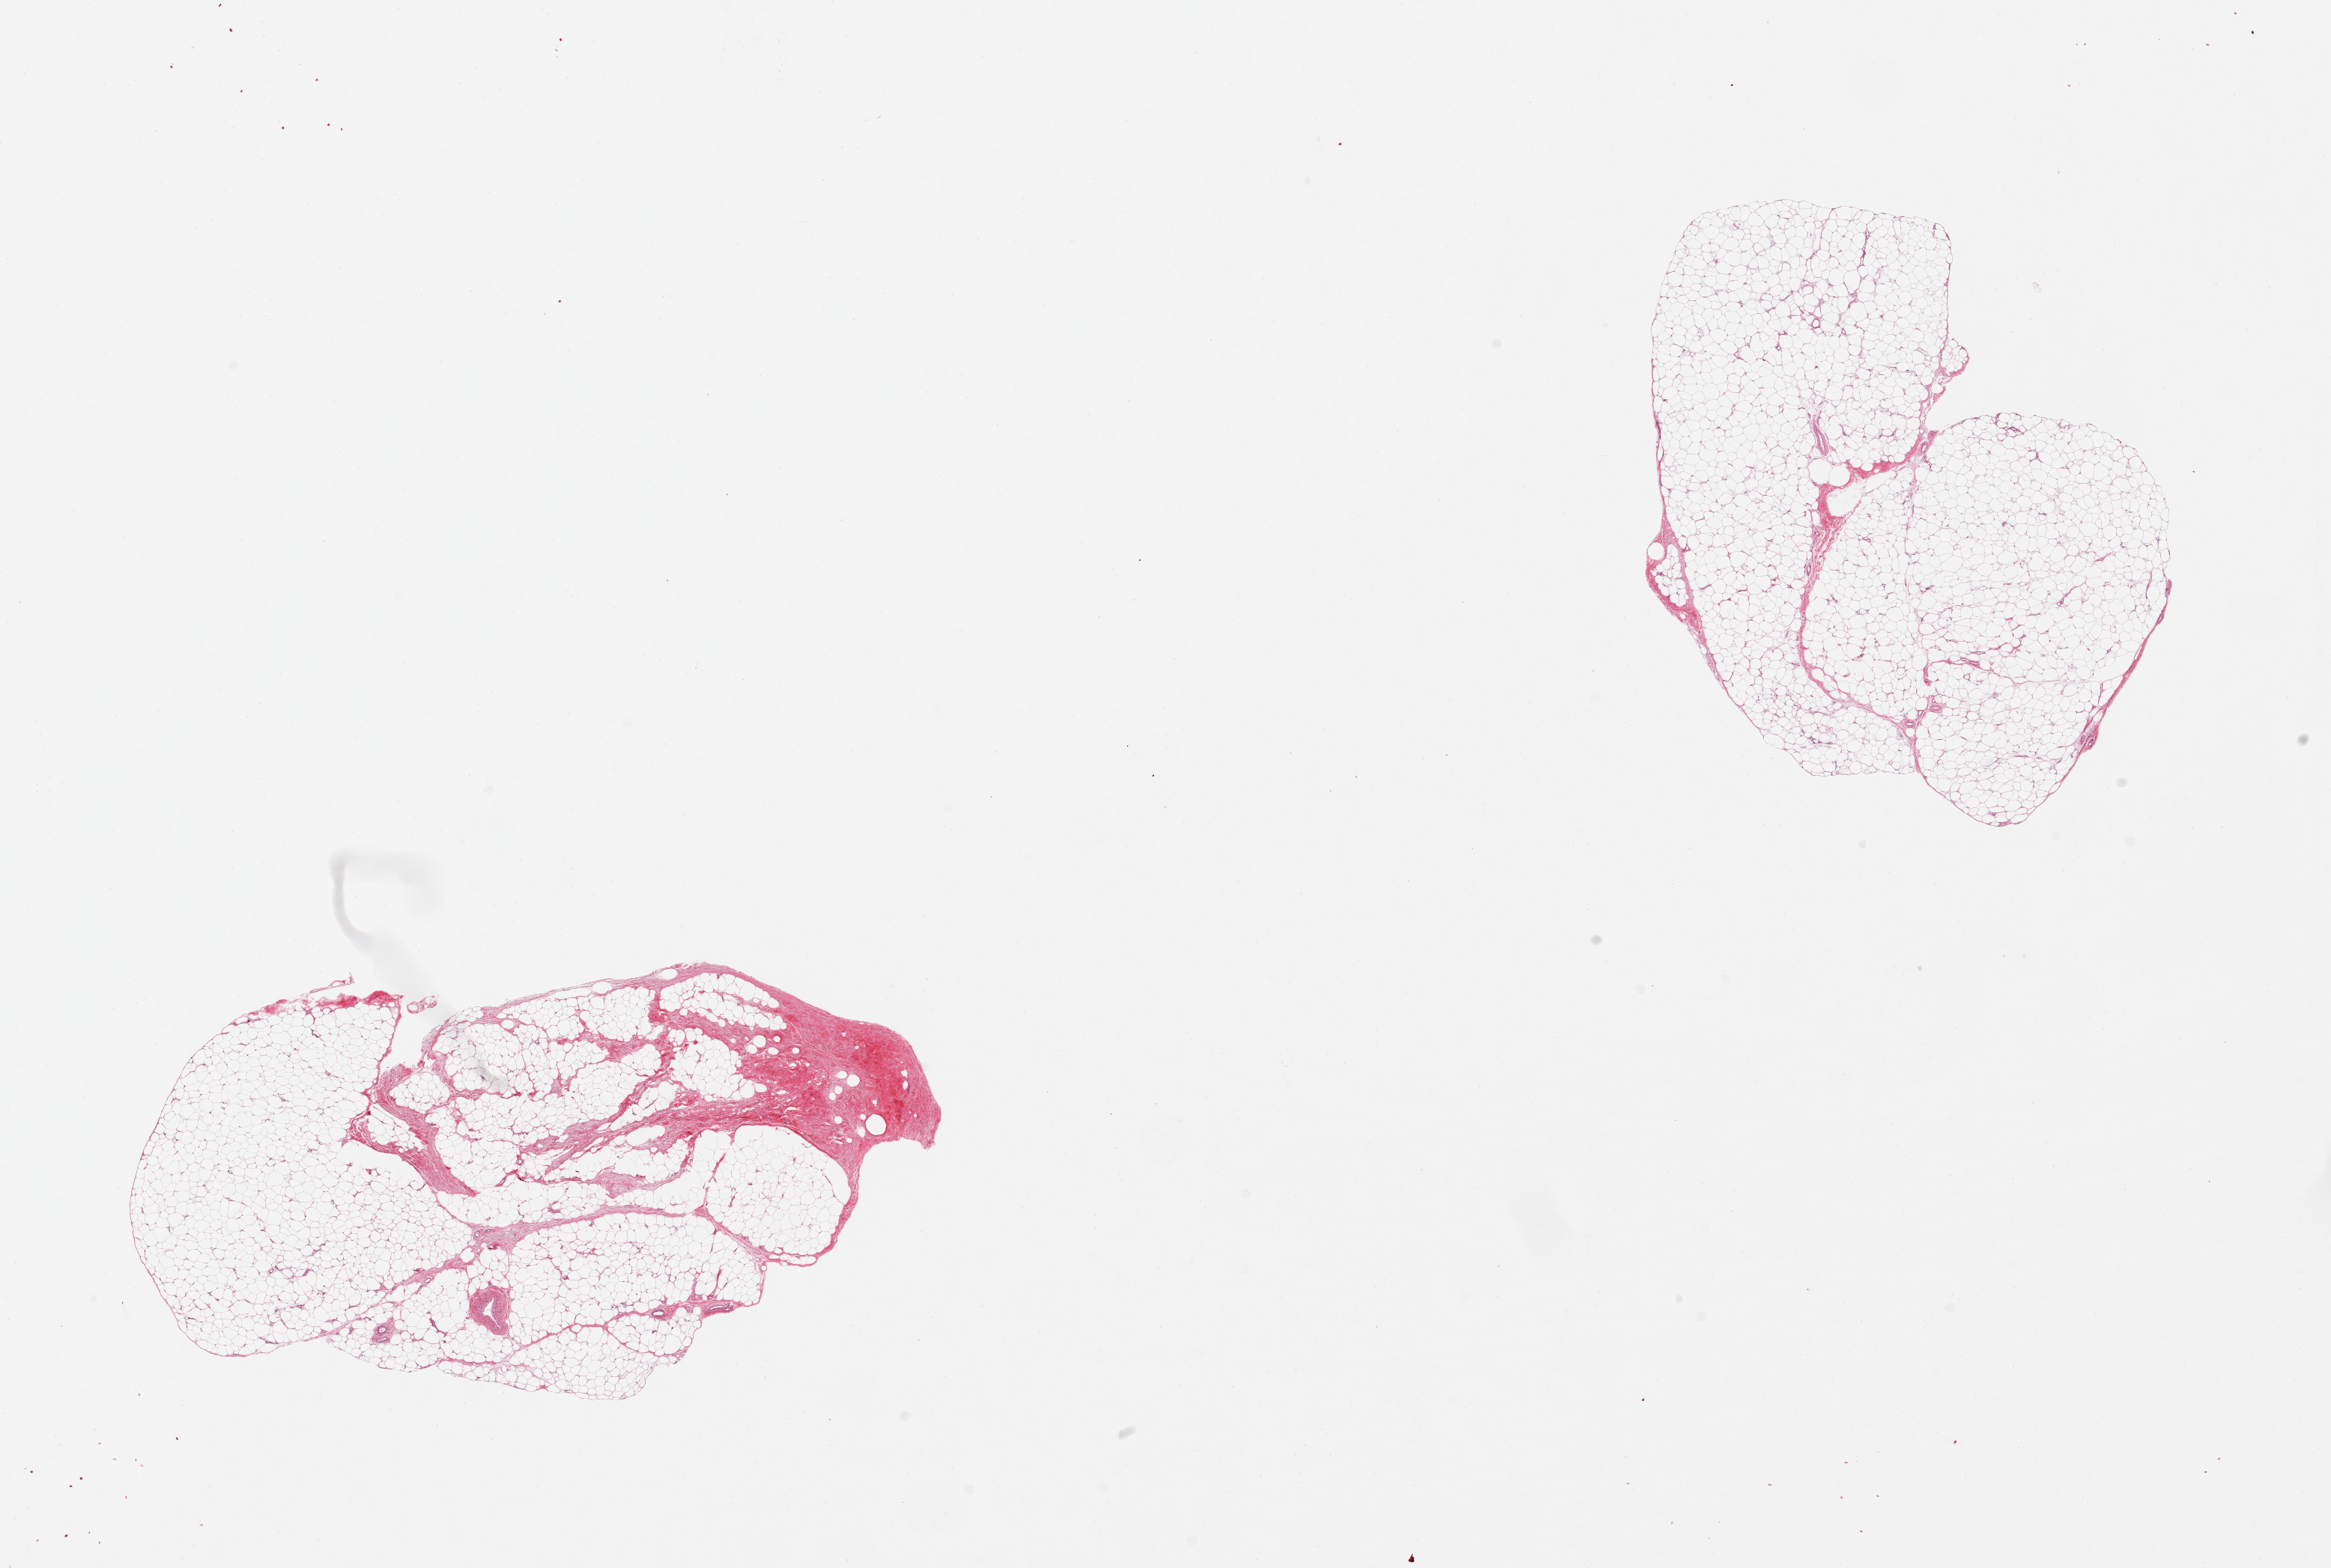
Whole-slide image, haematoxylin and eosin stain — low-resolution overview of the scanned area, about 24.6 x 16.6 mm (slide scanned at 20x), PAXgene-fixed paraffin-embedded (PFPE) section, section of adipose tissue (target tissue), donor tissue sample.
Pathologist's review note for this sample: 2 pieces; 1 piece has 10% fibrous tissue.